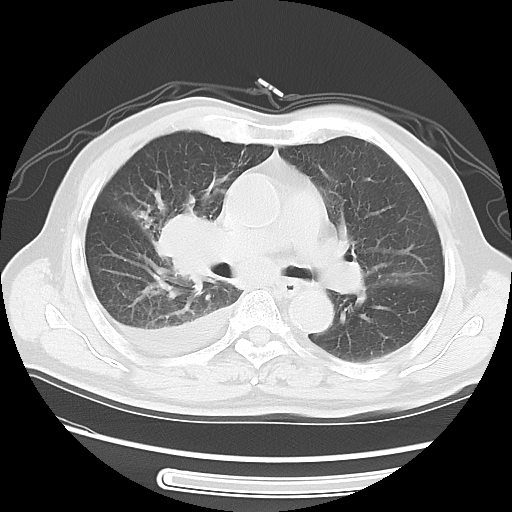
Chest CT, one axial slice. Position 32 of 56 along the scan axis. 120 kVp. Lung window (W 1500 / L -600 HU). 512 × 512 image matrix, field of view 360 × 360 mm. Male patient, age 77 years. Case-level facts recorded for this patient, not image findings: clinical TNM (as recorded): T3 N3 M1b; histopathological grade: G3.
Outlined on this slice (rectangle marked by the reading radiologist):
- lung tumour (recorded histology: small cell carcinoma): bounding box <147,203,231,292> (left, top, right, bottom; pixels)